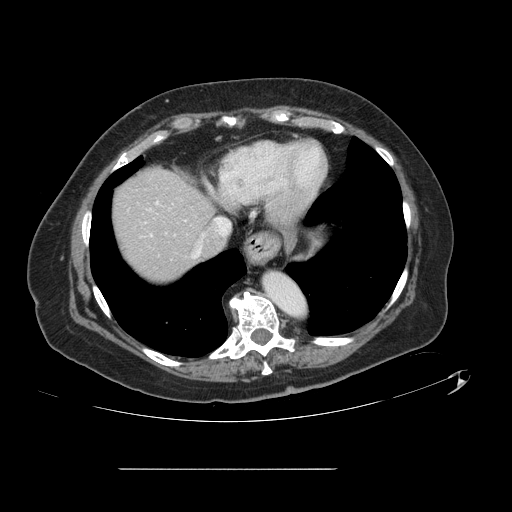
Contrast-enhanced abdominal CT, one axial slice; 120 kVp; soft-tissue window (W 400 / L 40 HU); 2.5 mm slice thickness; 512 × 512 image matrix. Female patient, age 75 years. Case-level facts recorded for this patient, not image findings: diagnosis: colorectal cancer liver metastases, imaged before liver resection; multiple liver metastases: no; largest metastasis: 2.4 cm; chemotherapy before resection: no.
Structures marked on this image (expert manual segmentation):
- hepatic veins: bounding box (x1, y1, x2, y2) in pixels: (193, 218, 230, 258)
- liver: (112, 168, 212, 283)
- planned liver remnant (the part of the liver to remain after resection): (112, 168, 212, 283)